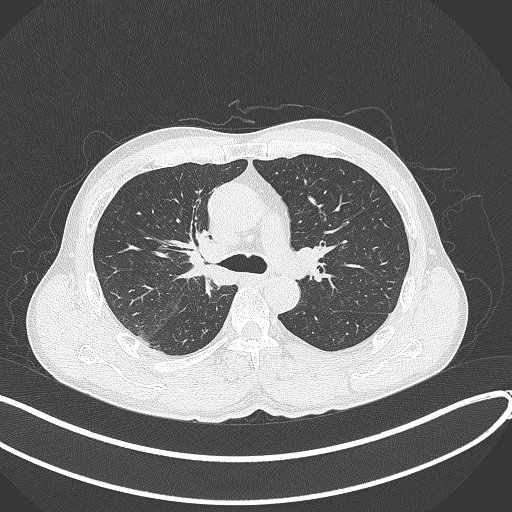
Chest CT, one axial slice. Slice 249 of 409 in the series (ordered by position). Reconstruction kernel B70f. Lung window (W 1500 / L -600 HU). 1 mm slice thickness. 512 × 512 image matrix, field of view 400 × 400 mm. Male patient, age 53 years. Case-level facts recorded for this patient, not image findings: clinical TNM (as recorded): T1b N0 M0.
Annotated regions visible in this slice (bounding box drawn by a radiologist):
- lung tumour (recorded histology: squamous cell carcinoma): box from (x=180, y=224) to (x=237, y=291) px